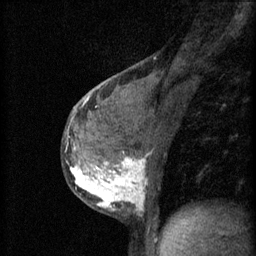
Breast MRI (dynamic contrast-enhanced), one sagittal slice; position 31 of 60 along the scan axis; 3 images stored at this slice position (order not interpretable as contrast timing); 1.5 T; TE 4.2 ms, TR 11 ms; 2 mm slice thickness; 256 × 256 image matrix, field of view 180 × 180 mm. Female patient, age 37 years.
Outlined on this slice (semi-automatic segmentation, software-assisted and operator-edited):
- analysis volume of interest (the breast-tissue region the enhancement analysis was run in; not a lesion): bounding box <66,138,157,215> (left, top, right, bottom; pixels)
- tumour enhancement mask (voxels above the 70 % enhancement threshold inside the analysis volume of interest): <66,154,147,211>